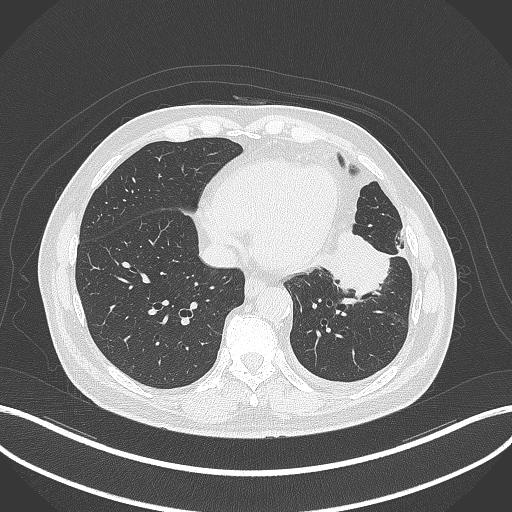
Chest CT, one axial slice. Position 112 of 230 along the scan axis. Reconstruction kernel B70f. Lung window (W 1500 / L -600 HU). 1 mm slice thickness. 512 × 512 image matrix. Patient: male, 68 years. From the clinical record (not read from this slice): clinical TNM (as recorded): T2b N0 M0.
Structures marked on this image (rectangle marked by the reading radiologist):
- lung tumour (recorded histology: squamous cell carcinoma): box from (x=316, y=228) to (x=394, y=302) px